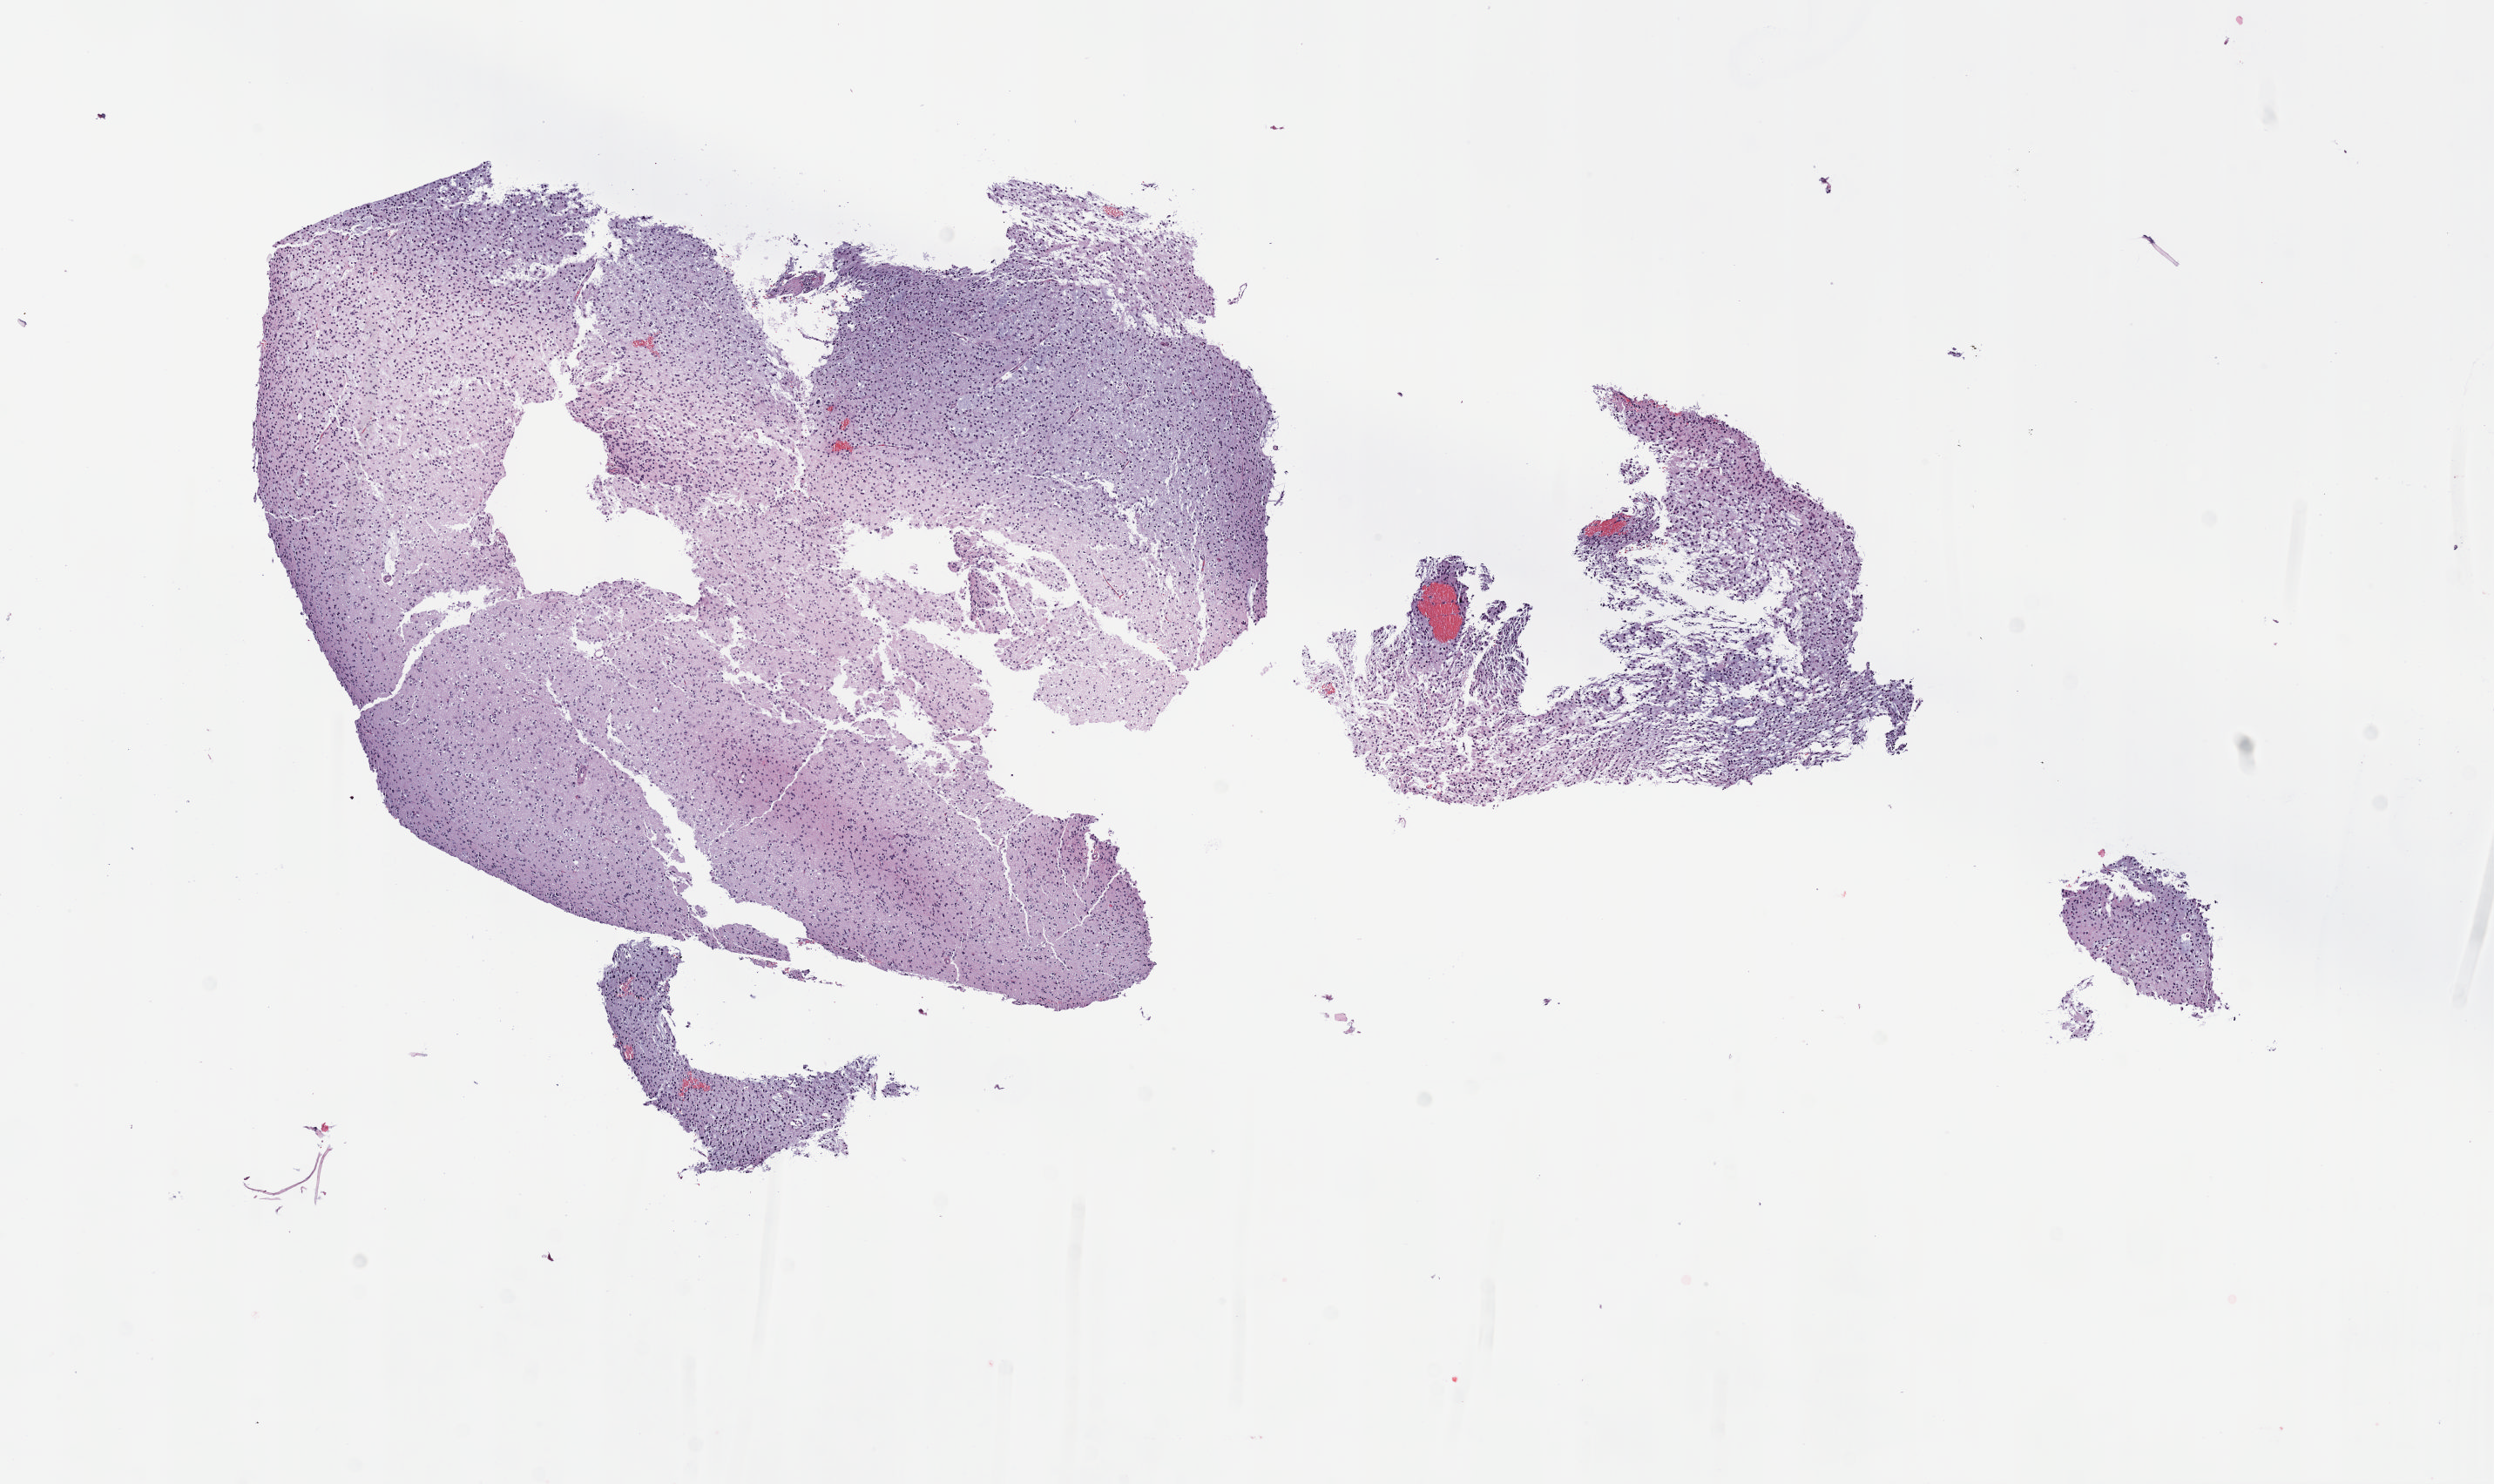
Whole-slide histology image, H&E — a low-resolution overview of the entire scanned area, about 11.6 x 6.9 mm (from a 40x scan), formalin-fixed paraffin-embedded (FFPE) diagnostic section, brain, primary tumour sample. Female patient; age at initial diagnosis 50 years. Histologic grade: G2 (moderately differentiated).
* pathologic diagnosis: Oligodendroglioma, NOS (cerebrum)
* laterality: right